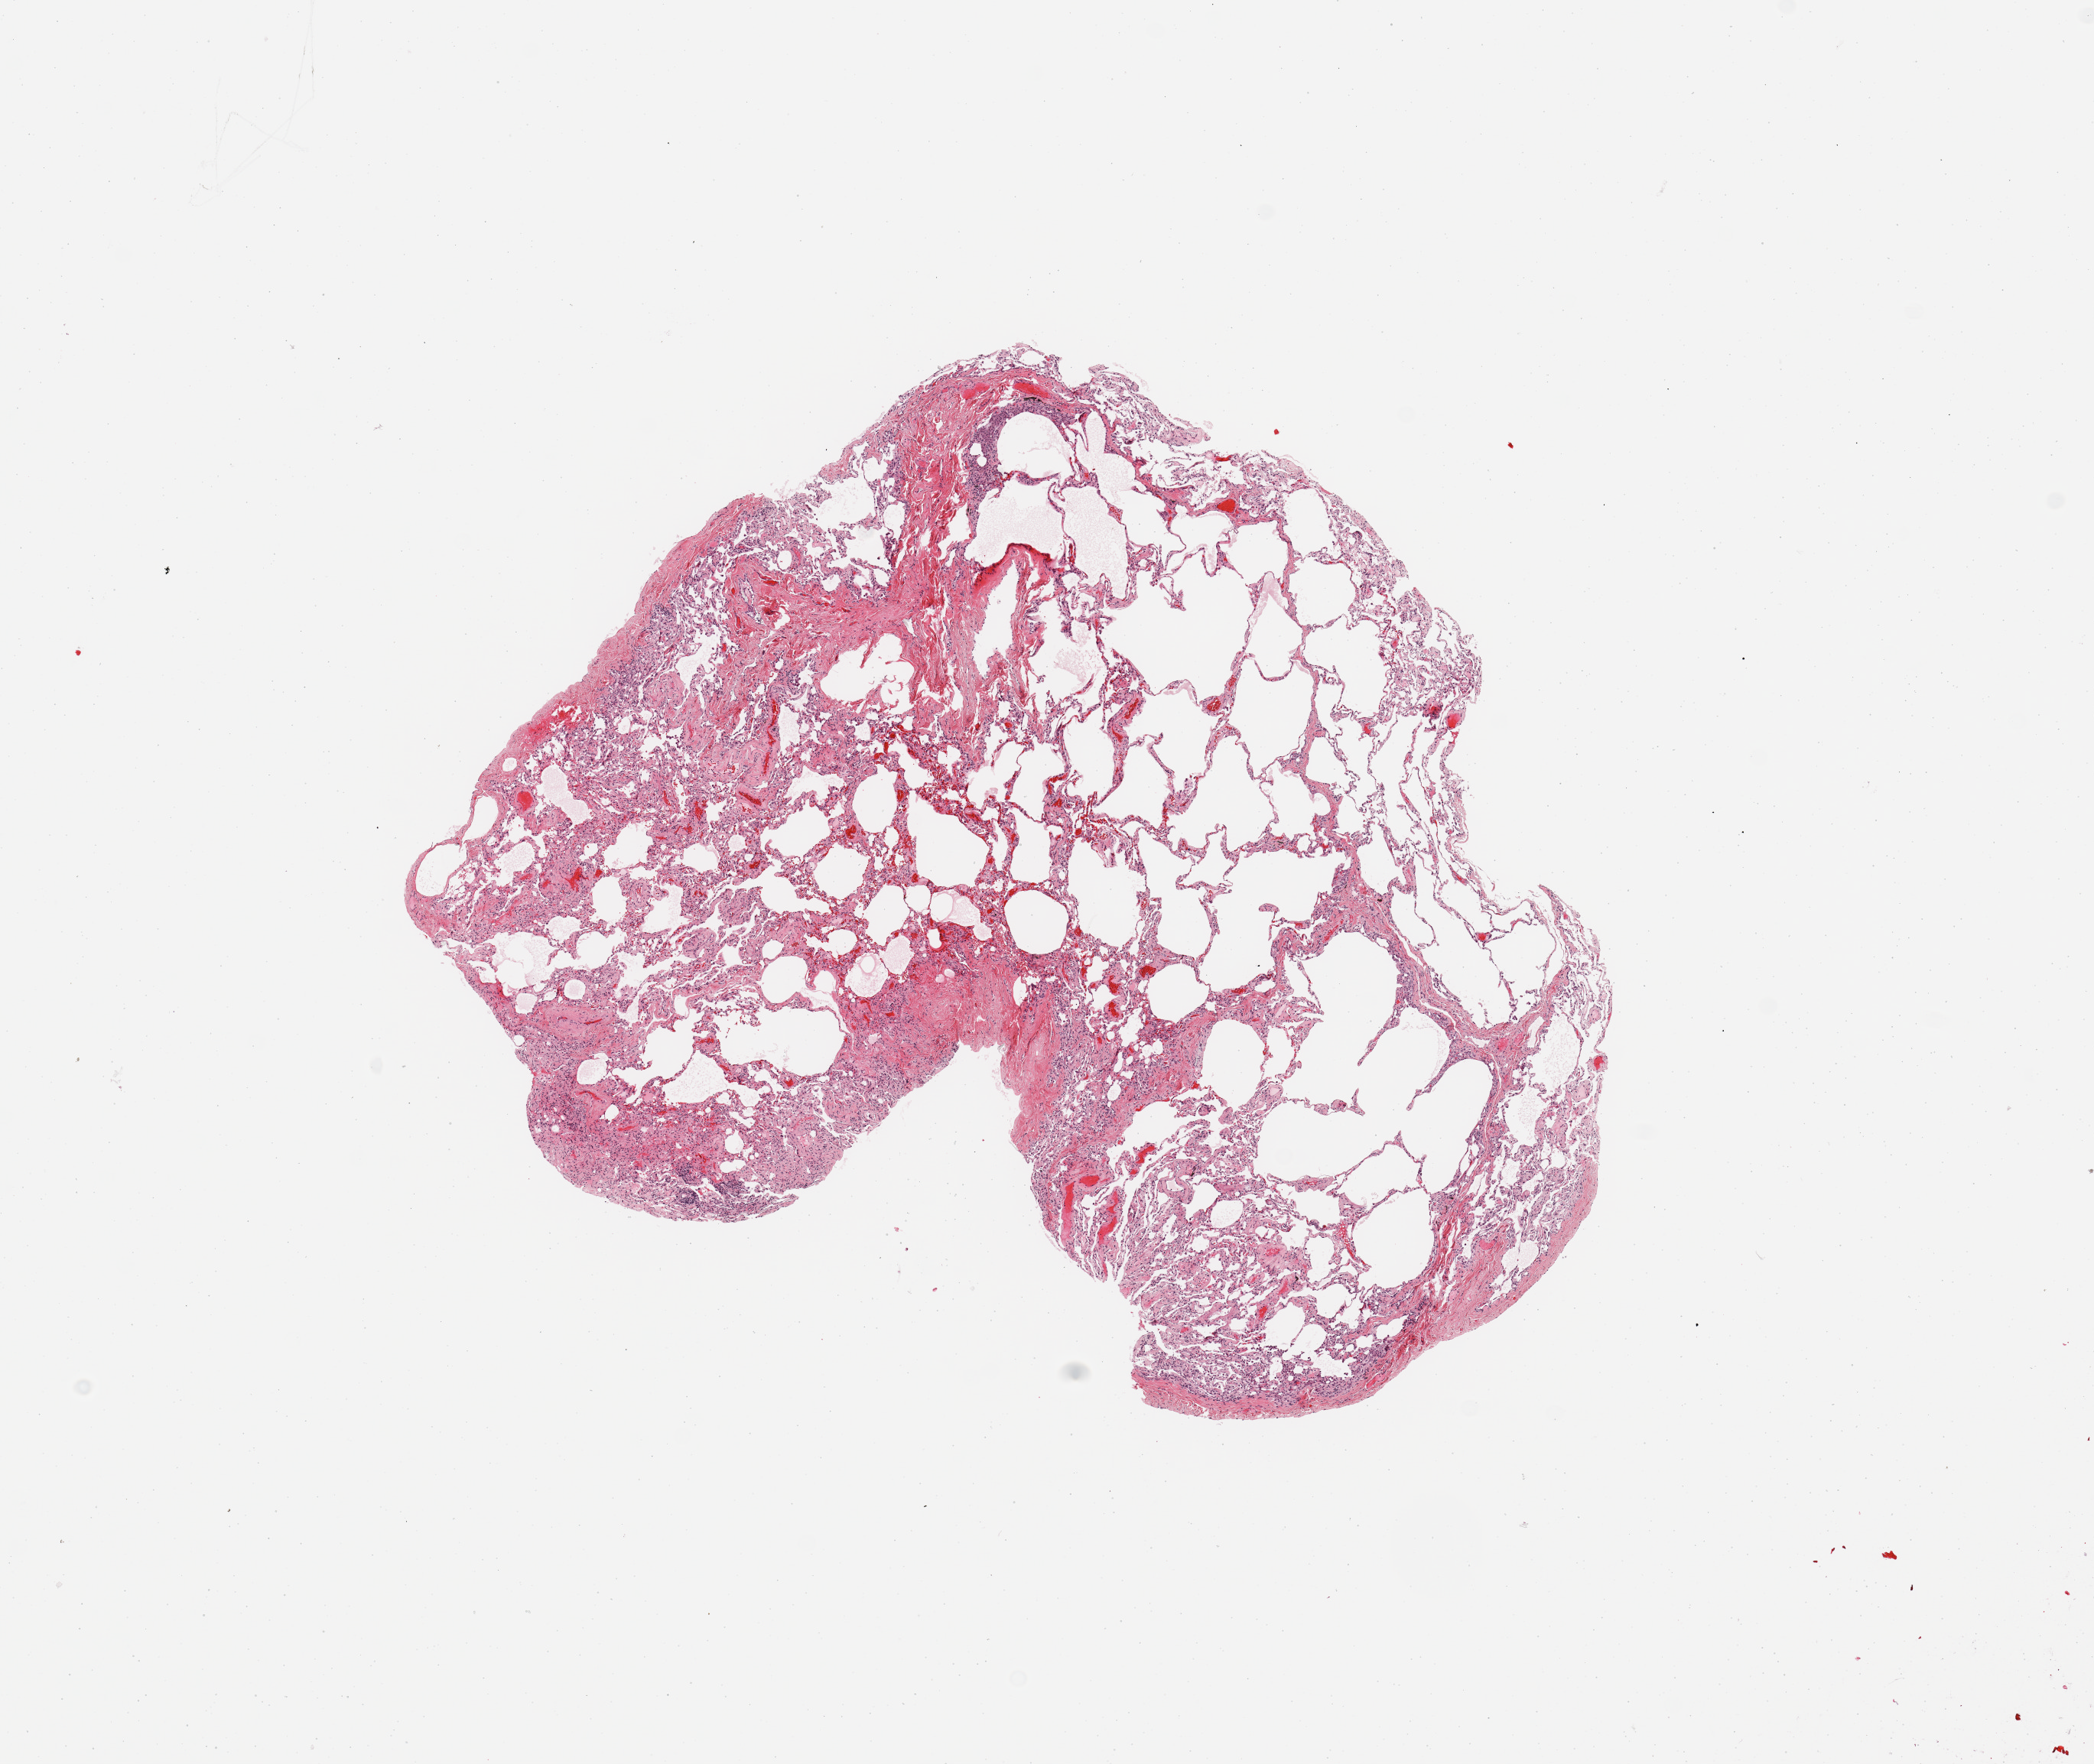
Whole-slide histology image, Hematoxylin and eosin (H&E) stained, low-resolution overview of the scanned area, about 10.8 x 9.1 mm (slide scanned at 20x); normal (non-tumour) tissue sample, sampled site: lung. Patient: female, age 61 years.
This section: normal (non-tumour) tissue from the same patient. Patient diagnosis: Adenocarcinoma, NOS.